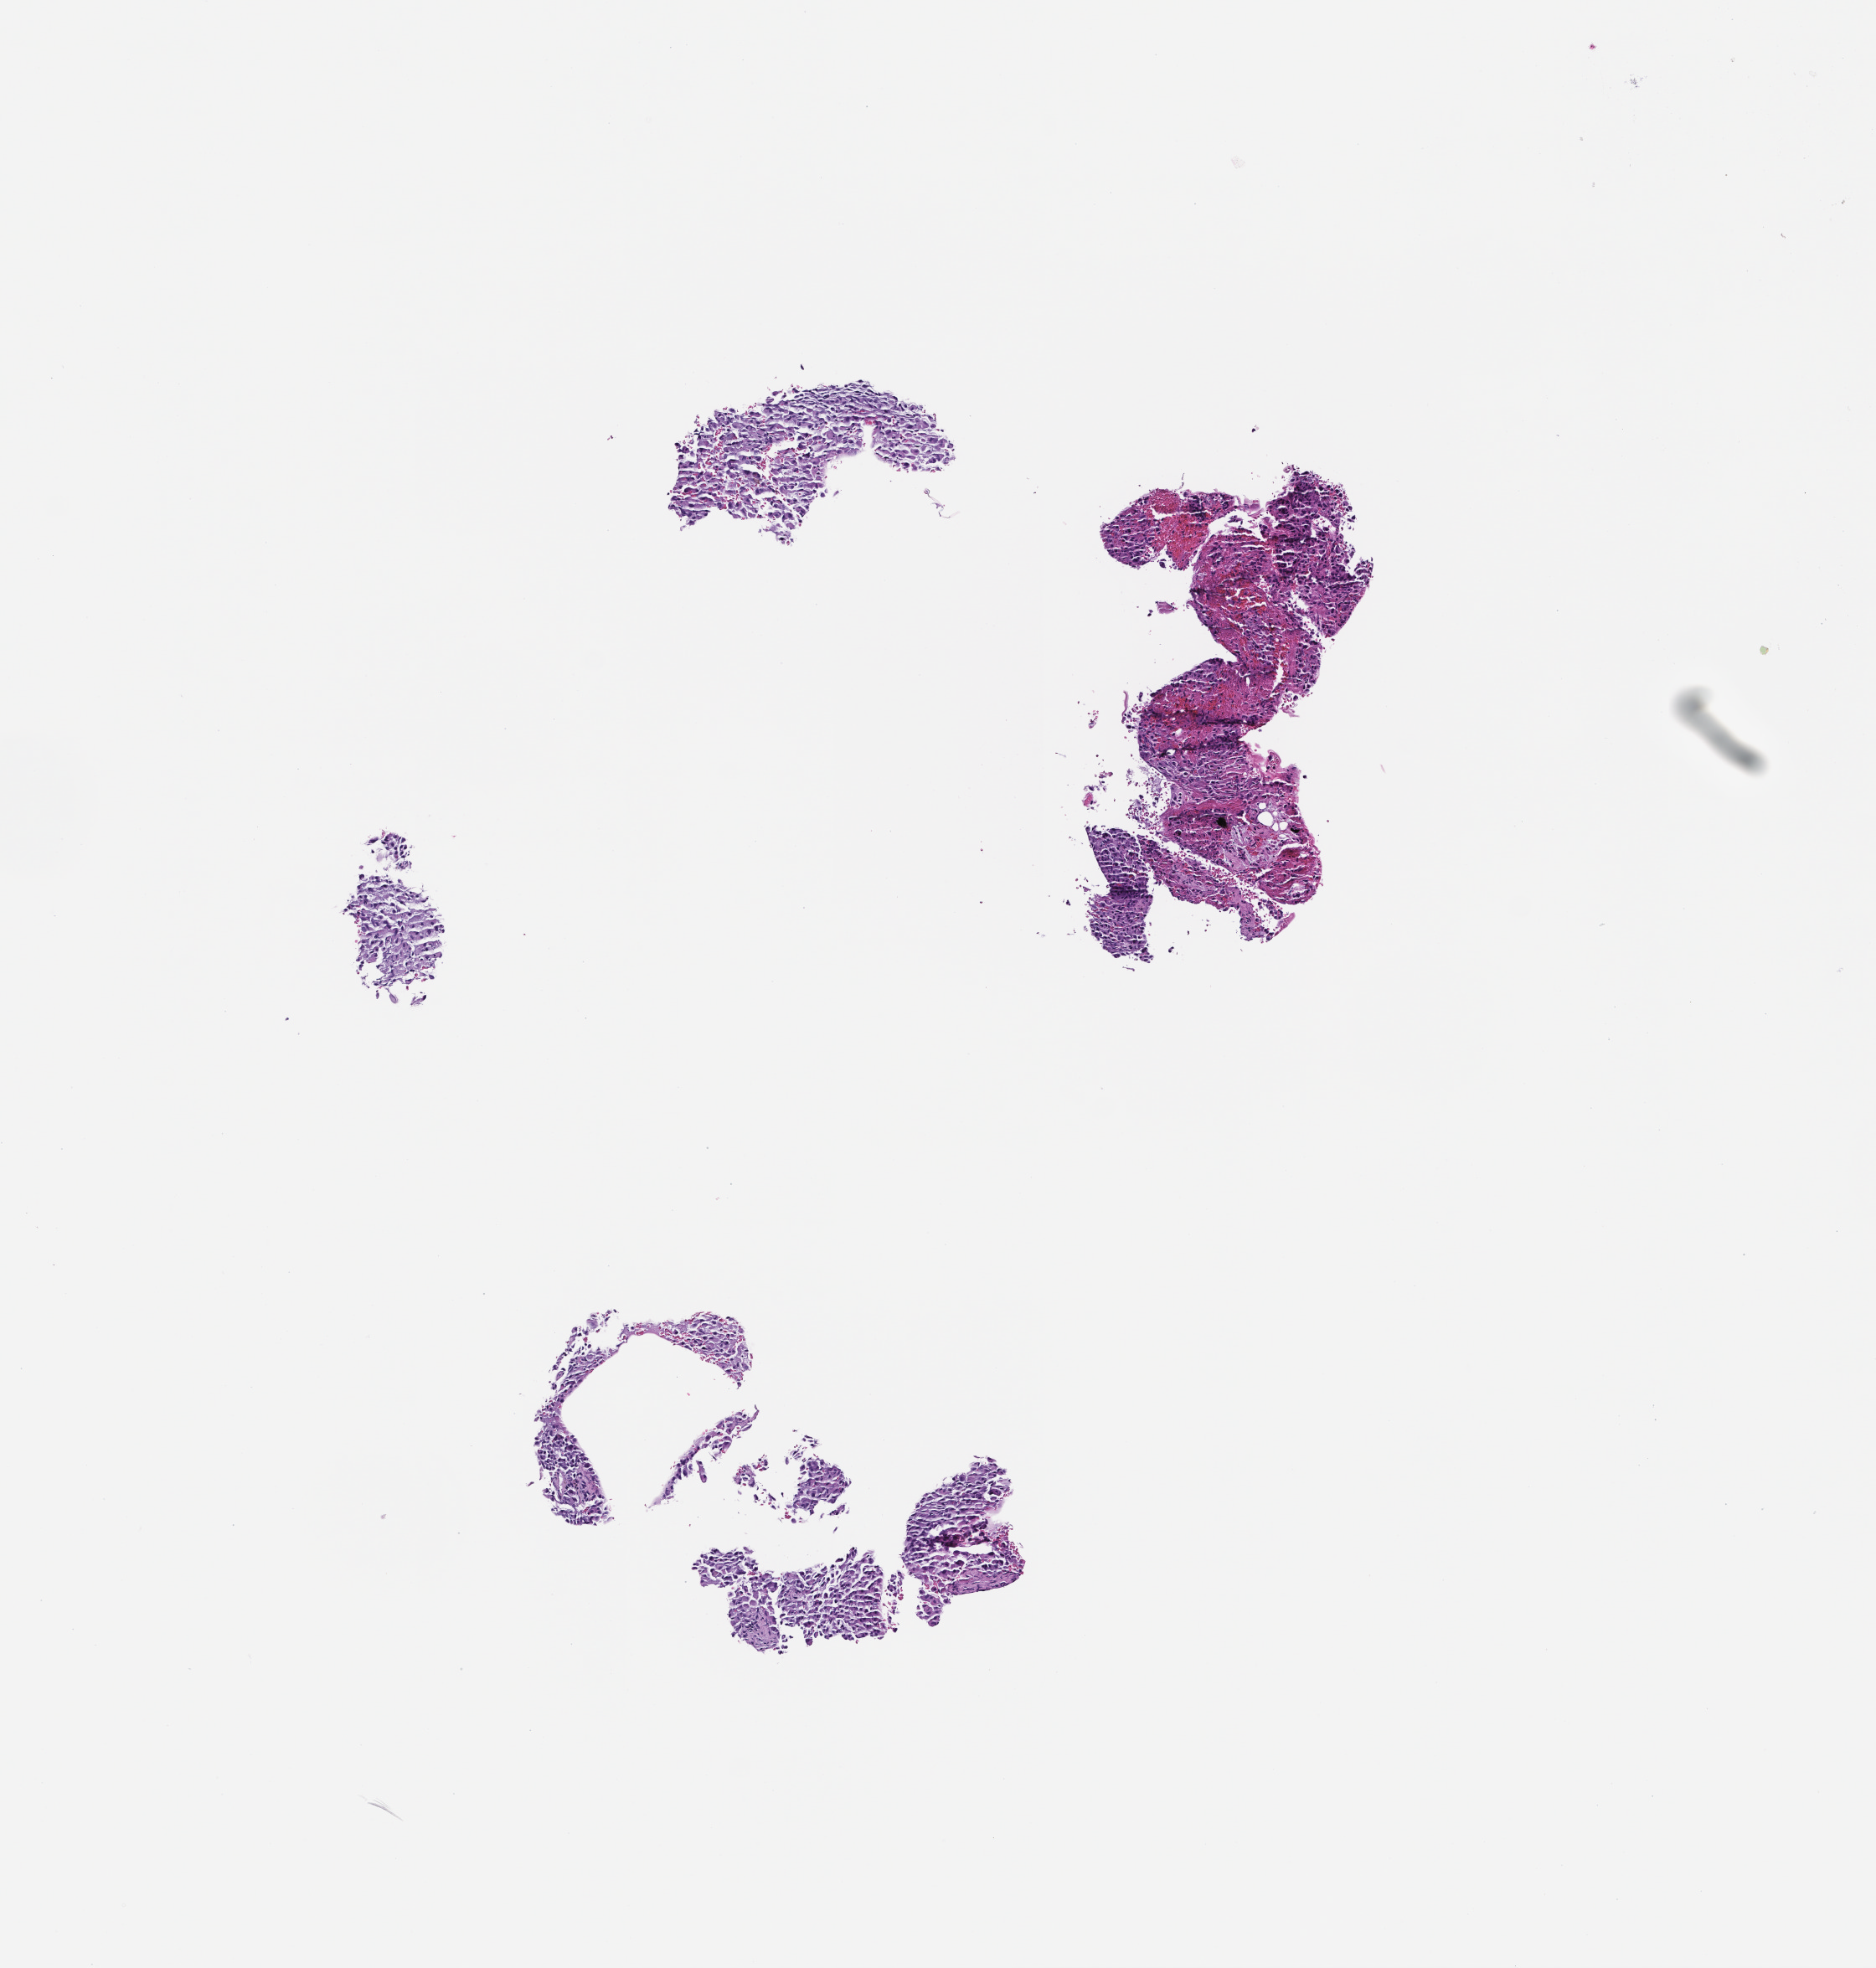
Hematoxylin and eosin (H&E) whole-slide image, whole scanned area (about 4.5 x 4.7 mm) shown as a low-resolution overview. Formalin-fixed, paraffin-embedded (FFPE) tissue. Collected at baseline (before treatment). Patient sex: male.
This section: metastasis (sampled organ not recorded). Patient diagnosis (primary): Melanoma.